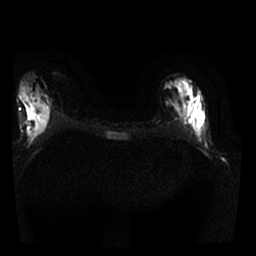
Breast MRI, one axial slice. Diffusion-weighted series; image 2 of 4 stored at this slice position (different b-values; order by instance number). 1.5 T. 4 mm slice thickness. 256 × 256 image matrix, field of view 300 × 300 mm. Female patient.
Annotated regions visible in this slice (expert manual segmentation):
- tumour on diffusion-weighted imaging: box from (x=185, y=94) to (x=203, y=136) px